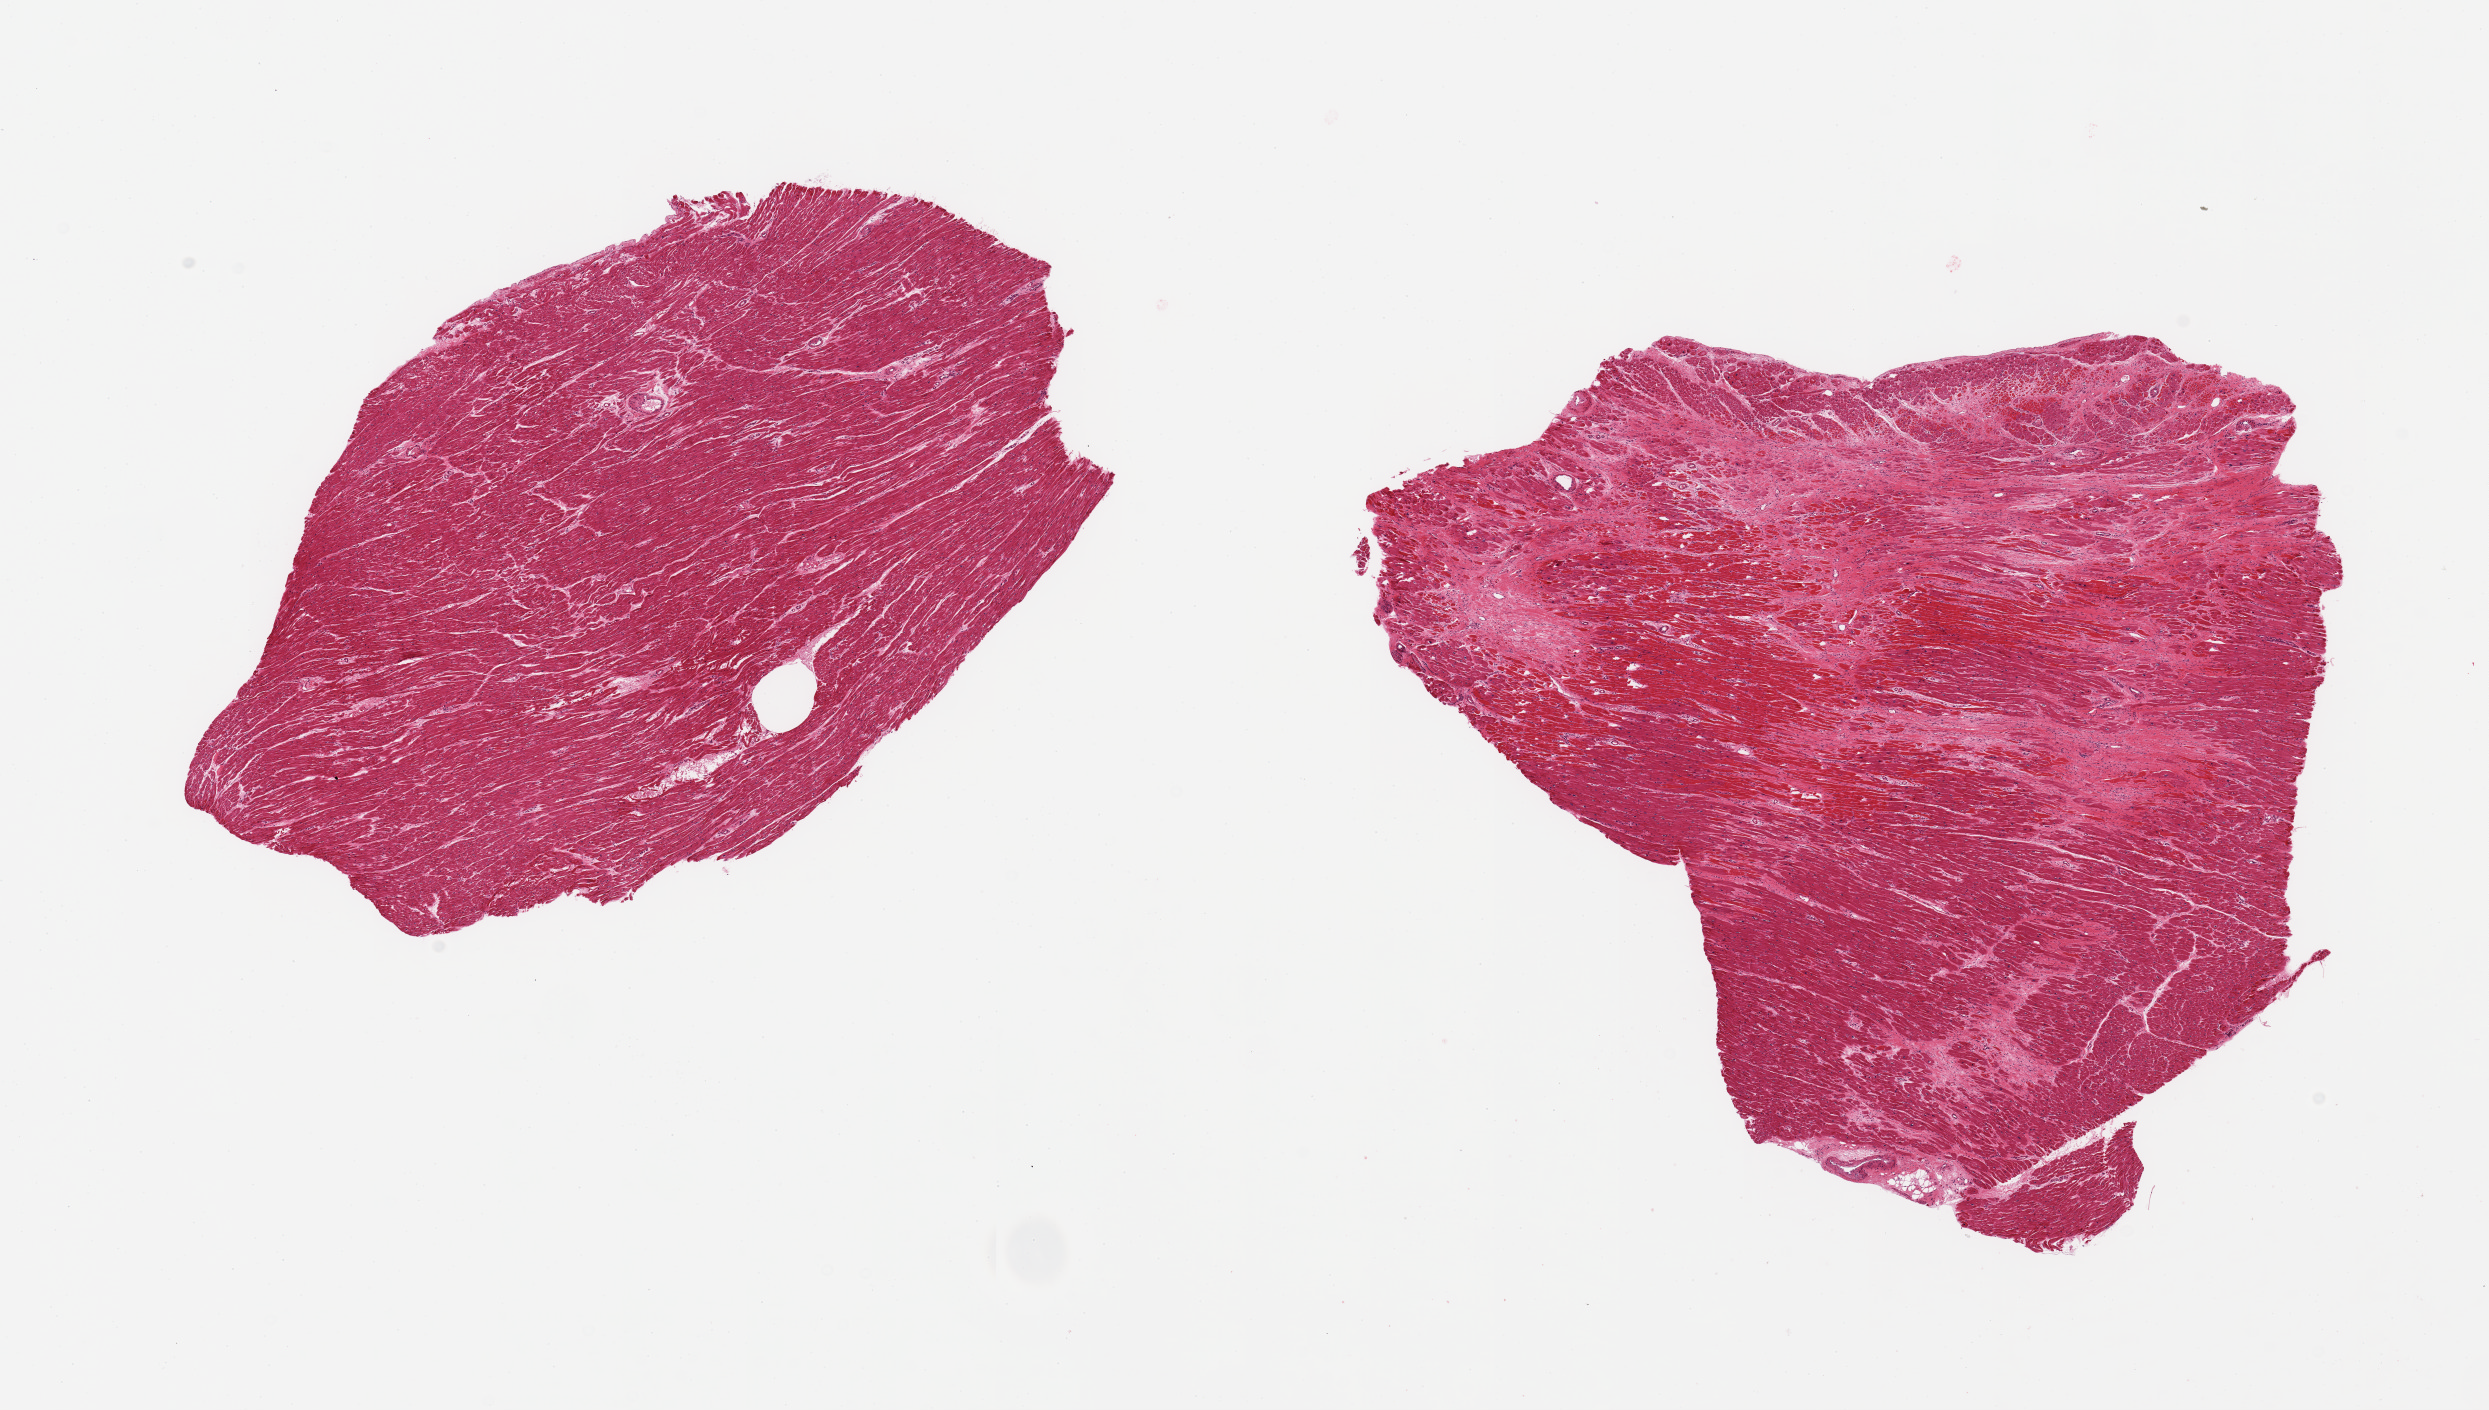
Whole-slide image, hematoxylin and eosin (H&E) stain, a low-resolution overview of the entire scanned area, about 19.7 x 11.2 mm. PAXgene-fixed paraffin-embedded (PFPE) section. Sampled site (target tissue): heart. Tissue donor sample.
Reviewer comment on this tissue sample: 2 pieces; 1 piece includes areas of acute extension of an older infarct, with hypereosinophilia and early coagulative necrosis surrounding patchy regions of scar.